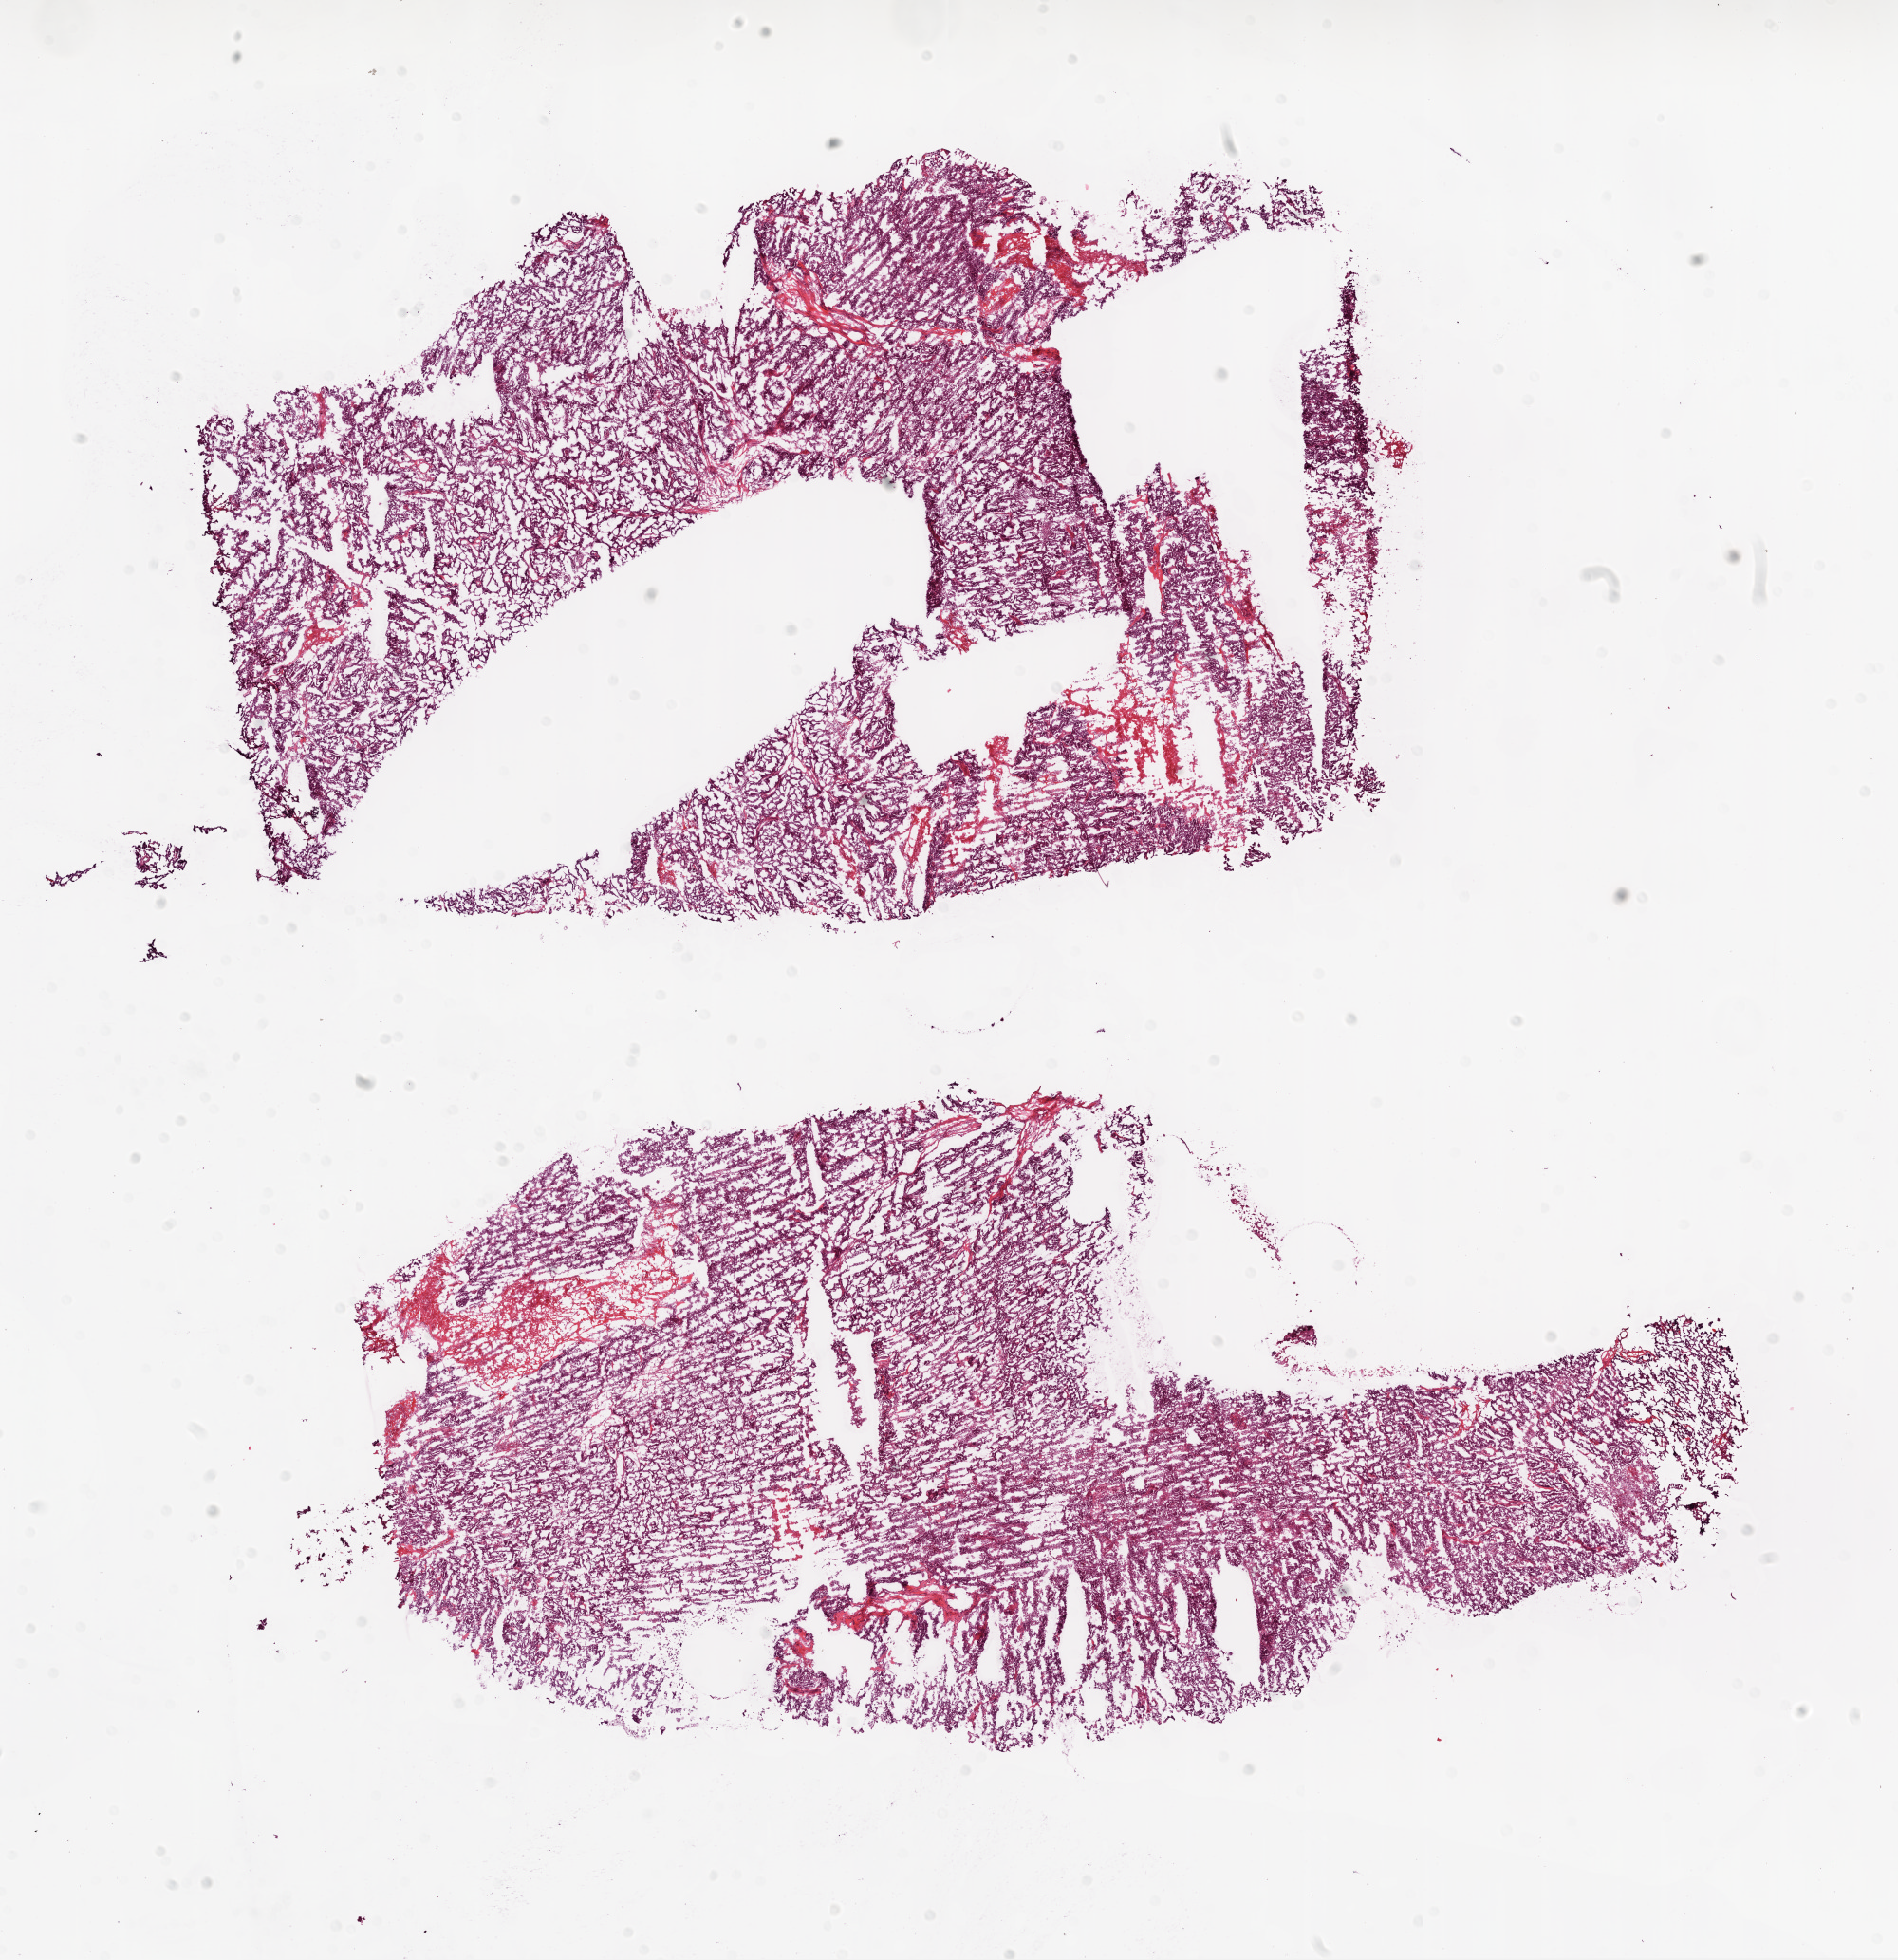
Digitized H&E-stained tissue section (whole slide) — a low-resolution overview of the entire scanned area, about 16.0 x 16.6 mm; frozen section; ovary, primary tumour sample. Female patient; age at initial diagnosis 69 years. Histologic grade: G2 (moderately differentiated). Slide review estimates, as recorded: tumour cells 90%, tumour nuclei 99%, normal cells 0%, stromal cells 5%, necrosis 5%.
- diagnosis: Serous cystadenocarcinoma, NOS
- FIGO stage: IIIC